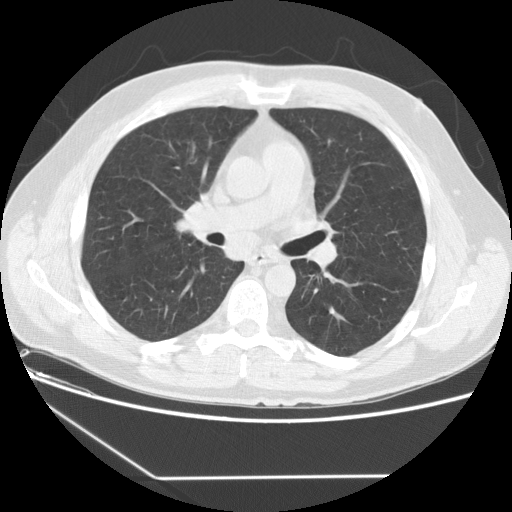
Low-dose screening chest CT, one axial slice; slice 85 of 154 in the series (ordered by position); reconstruction kernel STANDARD; 120 kVp; lung window (W 1500 / L -600 HU); 512 × 512 image matrix, field of view 370 × 370 mm.
Structures marked on this image (expert manual segmentation):
- lesion 1 (tumor, middle lobe of right lung): bounding box <174,217,191,234> (left, top, right, bottom; pixels)